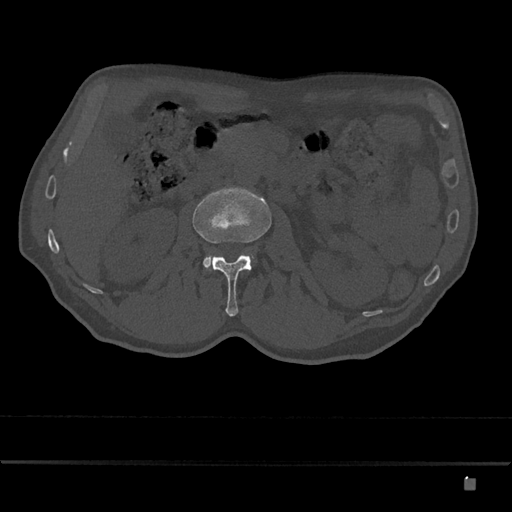
CT including the spine, one axial slice. Position 461 of 797 along the scan axis. 120 kVp. Bone window (W 1800 / L 400 HU). 0.5 mm slice thickness. 512 × 512 image matrix, field of view 390 × 390 mm. Patient: male, 72 years. From the clinical record (not read from this slice): primary cancer: prostate.
Annotated regions visible in this slice (semi-automatic segmentation, software-assisted and operator-edited):
- L2 vertebra: bounding box (x1, y1, x2, y2) in pixels: (192, 188, 272, 317)
- L3 vertebra: (203, 255, 254, 269)